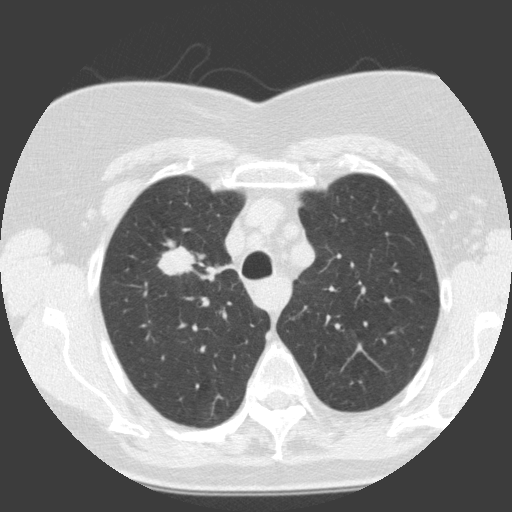
Low-dose screening chest CT, one axial slice. Position 112 of 146 along the scan axis. 120 kVp. Lung window (W 1500 / L -600 HU). 2 mm slice thickness. 512 × 512 image matrix, field of view 300 × 300 mm.
Annotated regions visible in this slice (expert manual segmentation):
- lesion 1 (tumor, upper lobe of right lung): bounding box (x1, y1, x2, y2) in pixels: (158, 246, 195, 276)